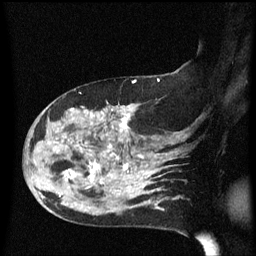
Breast MRI (dynamic contrast-enhanced), one sagittal slice. Slice 38 of 60 in the series (ordered by position). Dynamic contrast-enhanced series, image 2 of 3 at this slice position (ordered by acquisition). 1.5 T. TE 4.2 ms, TR 8.4 ms. 2.2 mm slice thickness. 256 × 256 image matrix. Female patient, age 47 years.
Outlined on this slice (semi-automatically segmented with operator editing):
- analysis volume of interest (the breast-tissue region the enhancement analysis was run in; not a lesion): bounding box <24,98,149,206> (left, top, right, bottom; pixels)
- tumour enhancement mask (voxels above the 70 % enhancement threshold inside the analysis volume of interest): <60,106,149,204>